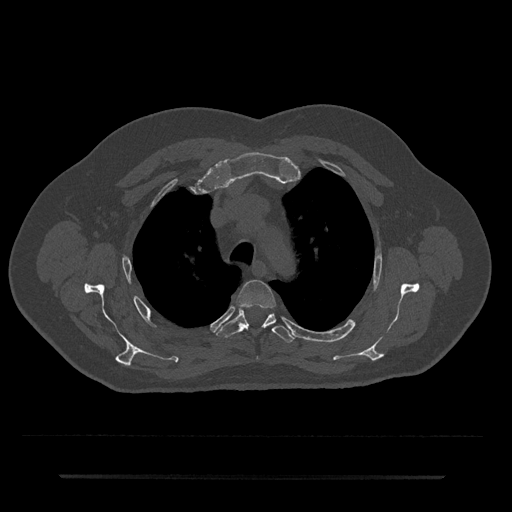
CT including the spine, one axial slice; slice 545 of 797 in the series (ordered by position); reconstruction kernel Br40s/3; bone window (W 1800 / L 400 HU); 0.5 mm slice thickness; 512 × 512 image matrix, field of view 437 × 437 mm. Male patient, age 69 years. From the clinical record (not read from this slice): primary cancer: prostate.
Structures marked on this image (semi-automatically segmented with operator editing):
- T3 vertebra: box from (x=237, y=280) to (x=276, y=308) px
- T4 vertebra: (x=217, y=308)–(x=294, y=343)